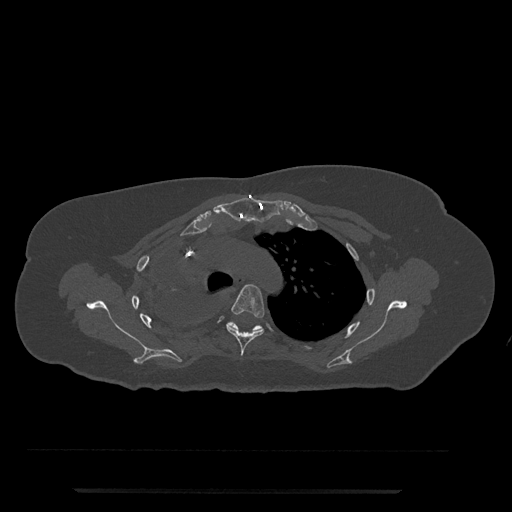
CT including the spine, one axial slice. Position 579 of 797 along the scan axis. 120 kVp. Bone window (W 1800 / L 400 HU). 512 × 512 image matrix, field of view 440 × 440 mm. Patient: female, 51 years. From the clinical record (not read from this slice): primary cancer: neuro; vertebrae with lytic lesions (as recorded): T8.
Outlined on this slice (semi-automatically segmented with operator editing):
- T4 vertebra: box from (x=226, y=284) to (x=265, y=356) px
- T5 vertebra: (x=226, y=322)–(x=264, y=333)